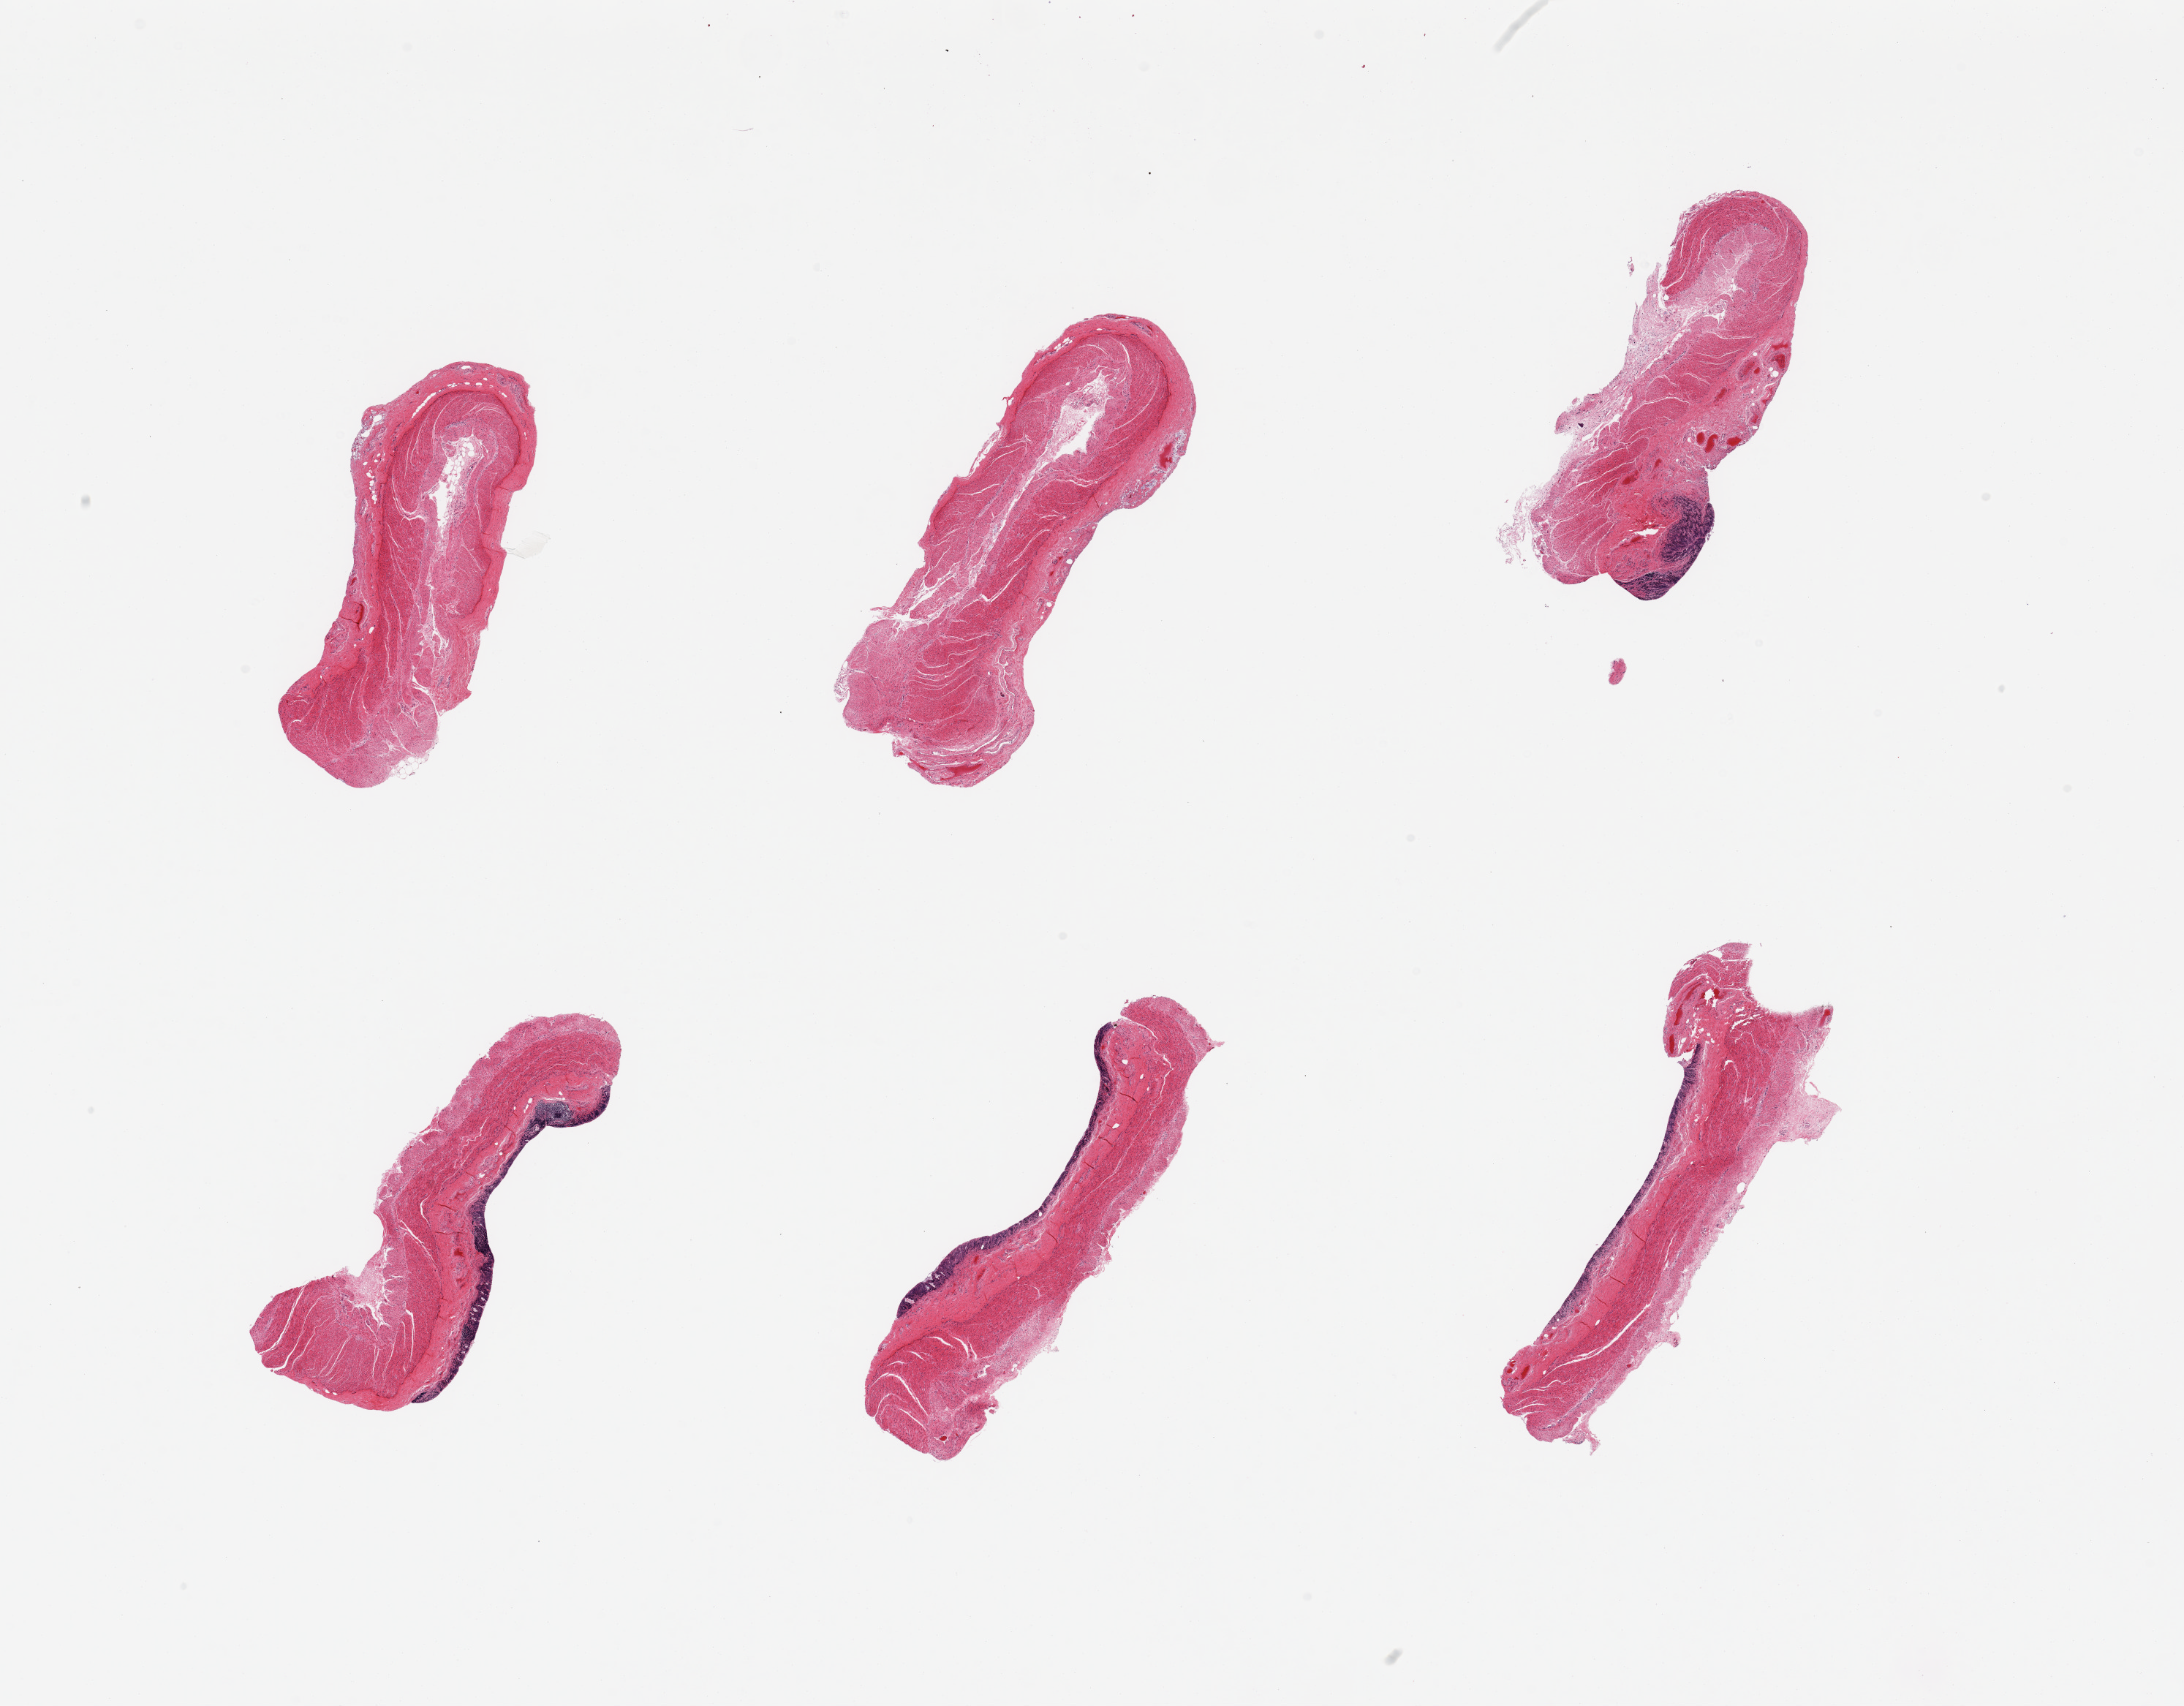
Hematoxylin and eosin (H&E) whole-slide image — whole scanned area (about 23.6 x 18.5 mm) shown as a low-resolution overview, PAXgene-fixed paraffin-embedded (PFPE) section, section of transverse colon (target tissue), tissue donor sample. Donor: female.
• review note (as recorded): 6 pieces, target mucosa up to ~0.15mm, glandular elements totally autolyzed